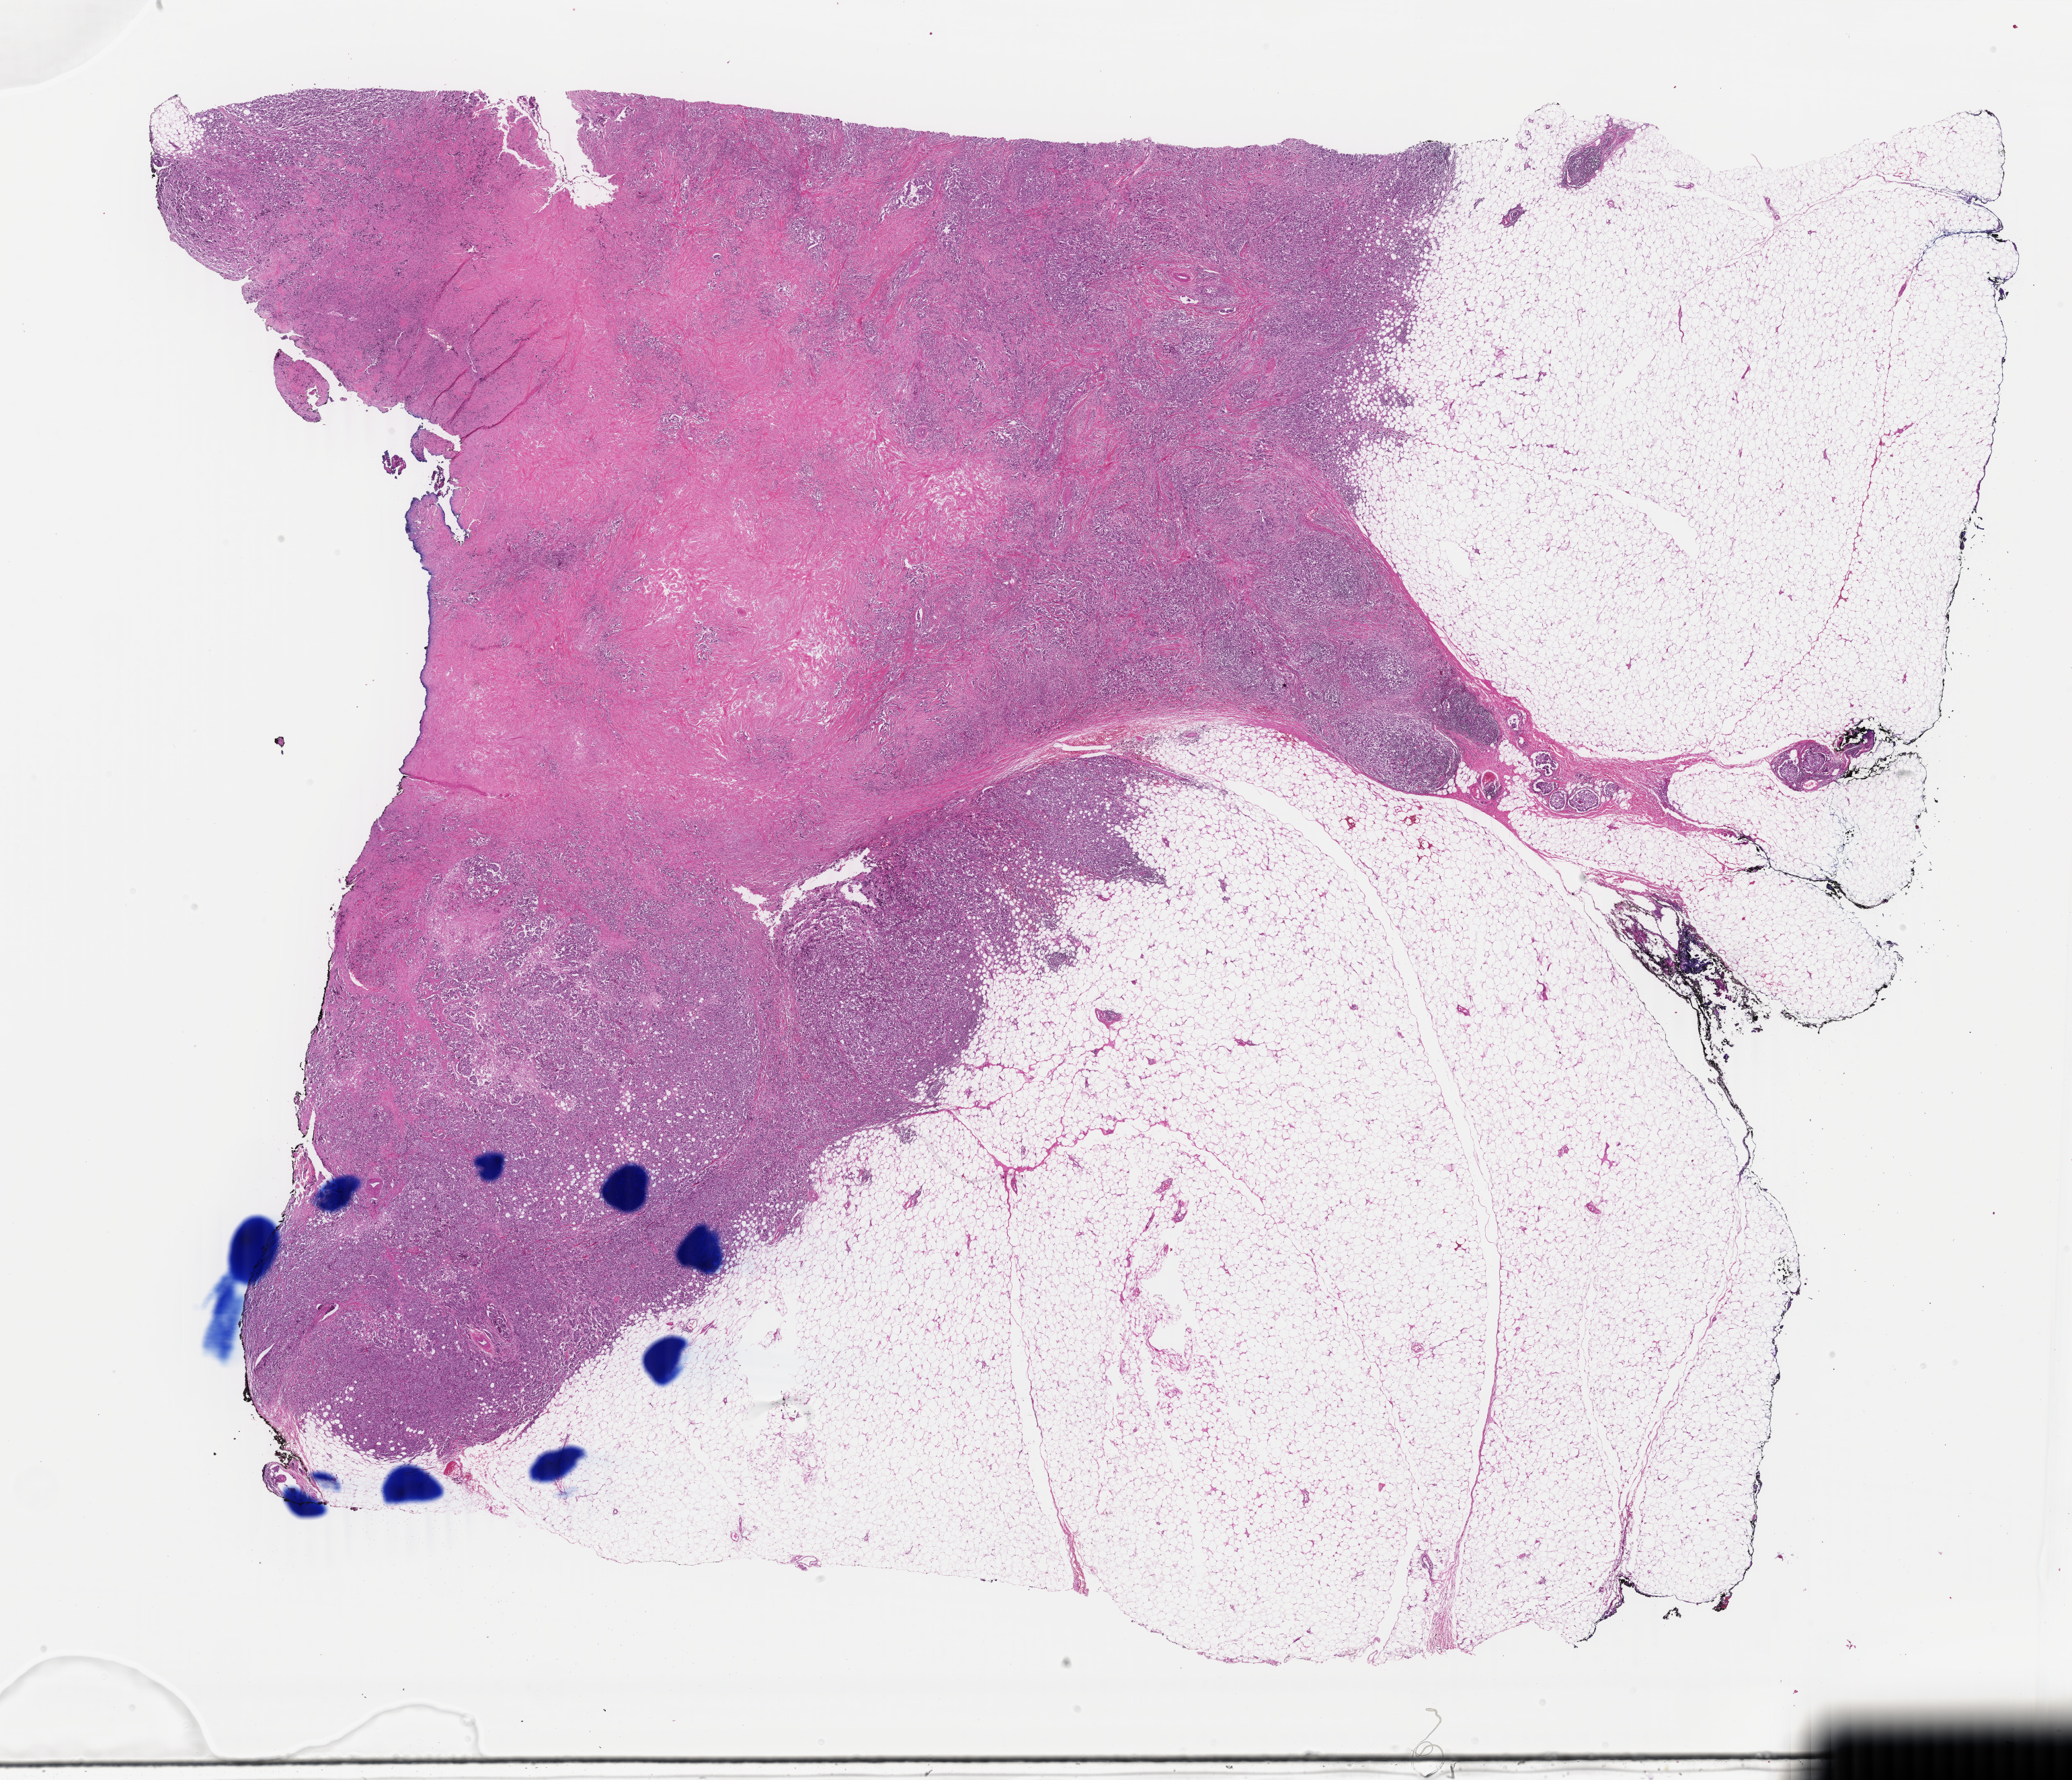
Digitized H&E tissue section (whole slide), shown as a low-resolution overview of the whole scanned area (about 24.5 x 21.1 mm), formalin-fixed paraffin-embedded (FFPE) diagnostic section, breast, primary tumour sample. Female patient; age at initial diagnosis 39 years.
AJCC pathologic stage: IIIA (4th edition). Lymph nodes positive (case pathology): 1 of 23 examined. Histologic diagnosis: Infiltrating duct carcinoma, NOS.